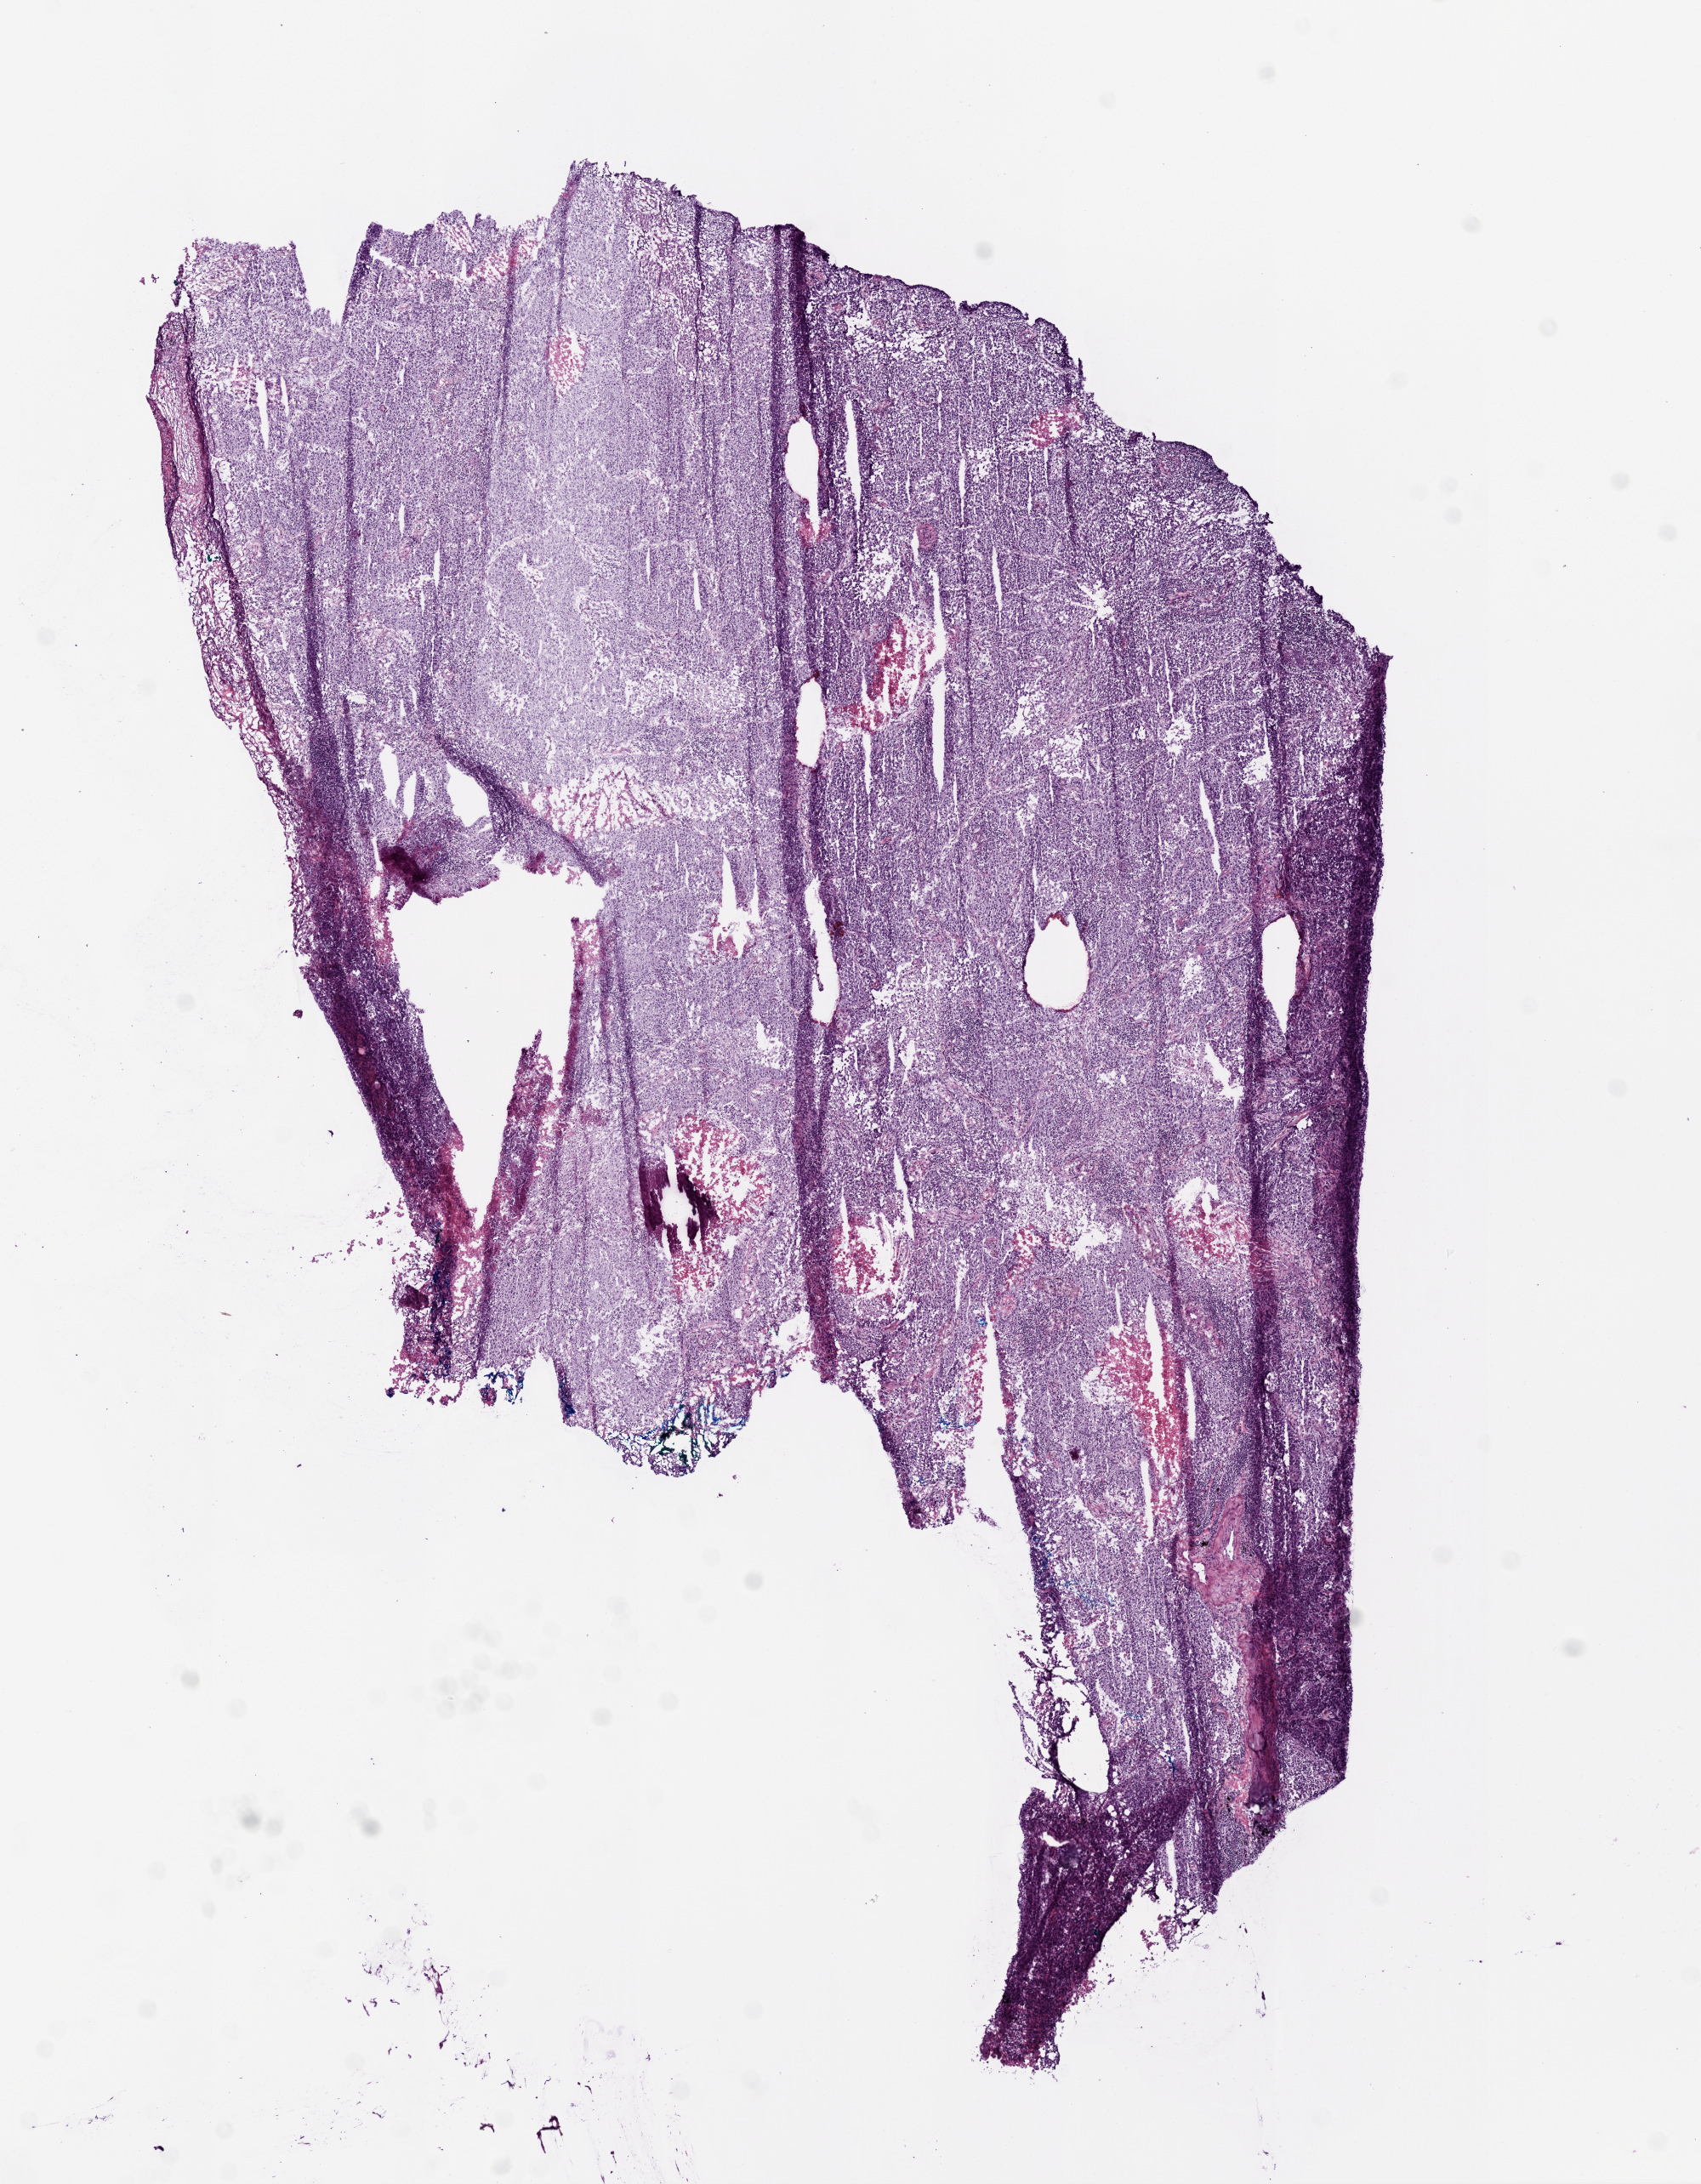
Hematoxylin and eosin (H&E) stained whole-slide image — shown as a low-resolution overview of the whole scanned area (about 8.0 x 10.3 mm, acquisition: 20x scan). Frozen section from the top of the tissue portion. Sample: primary tumour, lung. Patient: female, age at initial diagnosis 73 years.
Diagnosis: Adenocarcinoma, NOS (upper lobe, lung).